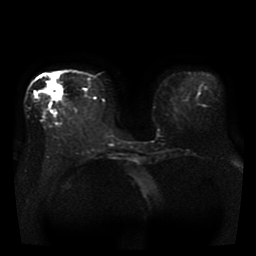
Breast MRI, one axial slice. Slice 13 of 41 in the series (ordered by position). Diffusion-weighted series; image 2 of 4 stored at this slice position (different b-values; order by instance number). 1.5 T. 5 mm slice thickness. 256 × 256 image matrix, field of view 330 × 330 mm. Female patient.
Annotated regions visible in this slice (manually delineated by an expert):
- tumour on diffusion-weighted imaging: box from (x=46, y=82) to (x=62, y=99) px